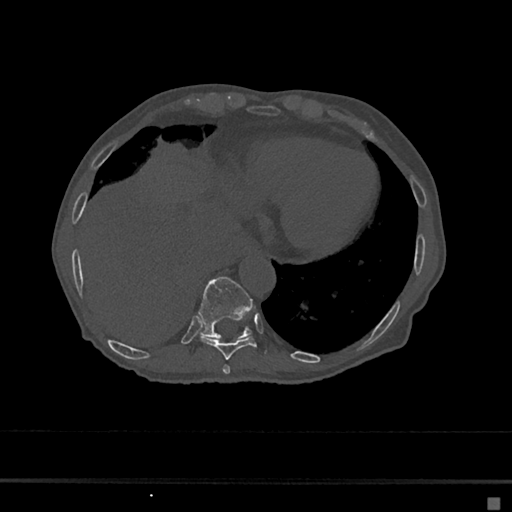
CT including the spine, one axial slice; slice 254 of 797 in the series (ordered by position); bone window (W 1800 / L 400 HU); 512 × 512 image matrix. Patient: female, 68 years. From the clinical record (not read from this slice): primary cancer: renal.
Annotated regions visible in this slice (semi-automatically segmented with operator editing):
- T10 vertebra: bounding box (x1, y1, x2, y2) in pixels: (198, 277, 253, 339)
- T8 vertebra: (222, 364, 231, 375)
- T9 vertebra: (200, 336, 265, 360)